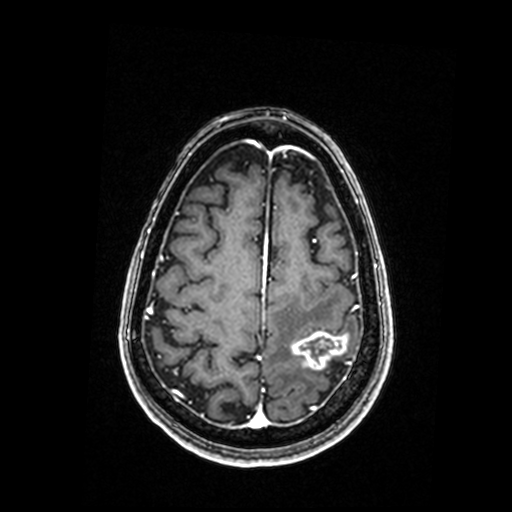
Brain MRI from a brain-tumour surgery series, one axial slice; slice 53 of 192 in the series (ordered by position); T1-weighted post-contrast; 0.98 mm slice thickness; 512 × 512 image matrix, field of view 250 × 250 mm. Case-level facts recorded for this patient, not image findings: histopathology: Metastastic Carcinoma, Poorly Differentiated; tumour location: Left Parietal.
Outlined on this slice (expert manual segmentation):
- tumour: bounding box <292,332,348,369> (left, top, right, bottom; pixels)